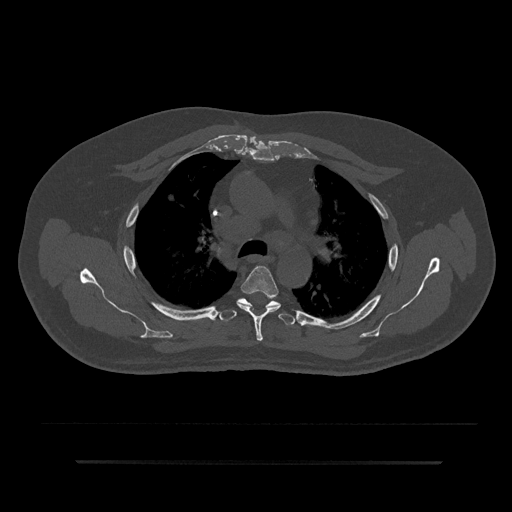
CT including the spine, one axial slice. Position 603 of 797 along the scan axis. Reconstruction kernel Br40s/3. 120 kVp. Bone window (W 1800 / L 400 HU). 0.5 mm slice thickness. 512 × 512 image matrix, field of view 464 × 464 mm. Patient: male, 59 years. Case-level facts recorded for this patient, not image findings: primary cancer: bile ducts.
Annotated regions visible in this slice (semi-automatic segmentation, software-assisted and operator-edited):
- T4 vertebra: bounding box (x1, y1, x2, y2) in pixels: (237, 266, 281, 342)
- T5 vertebra: (219, 298, 297, 325)